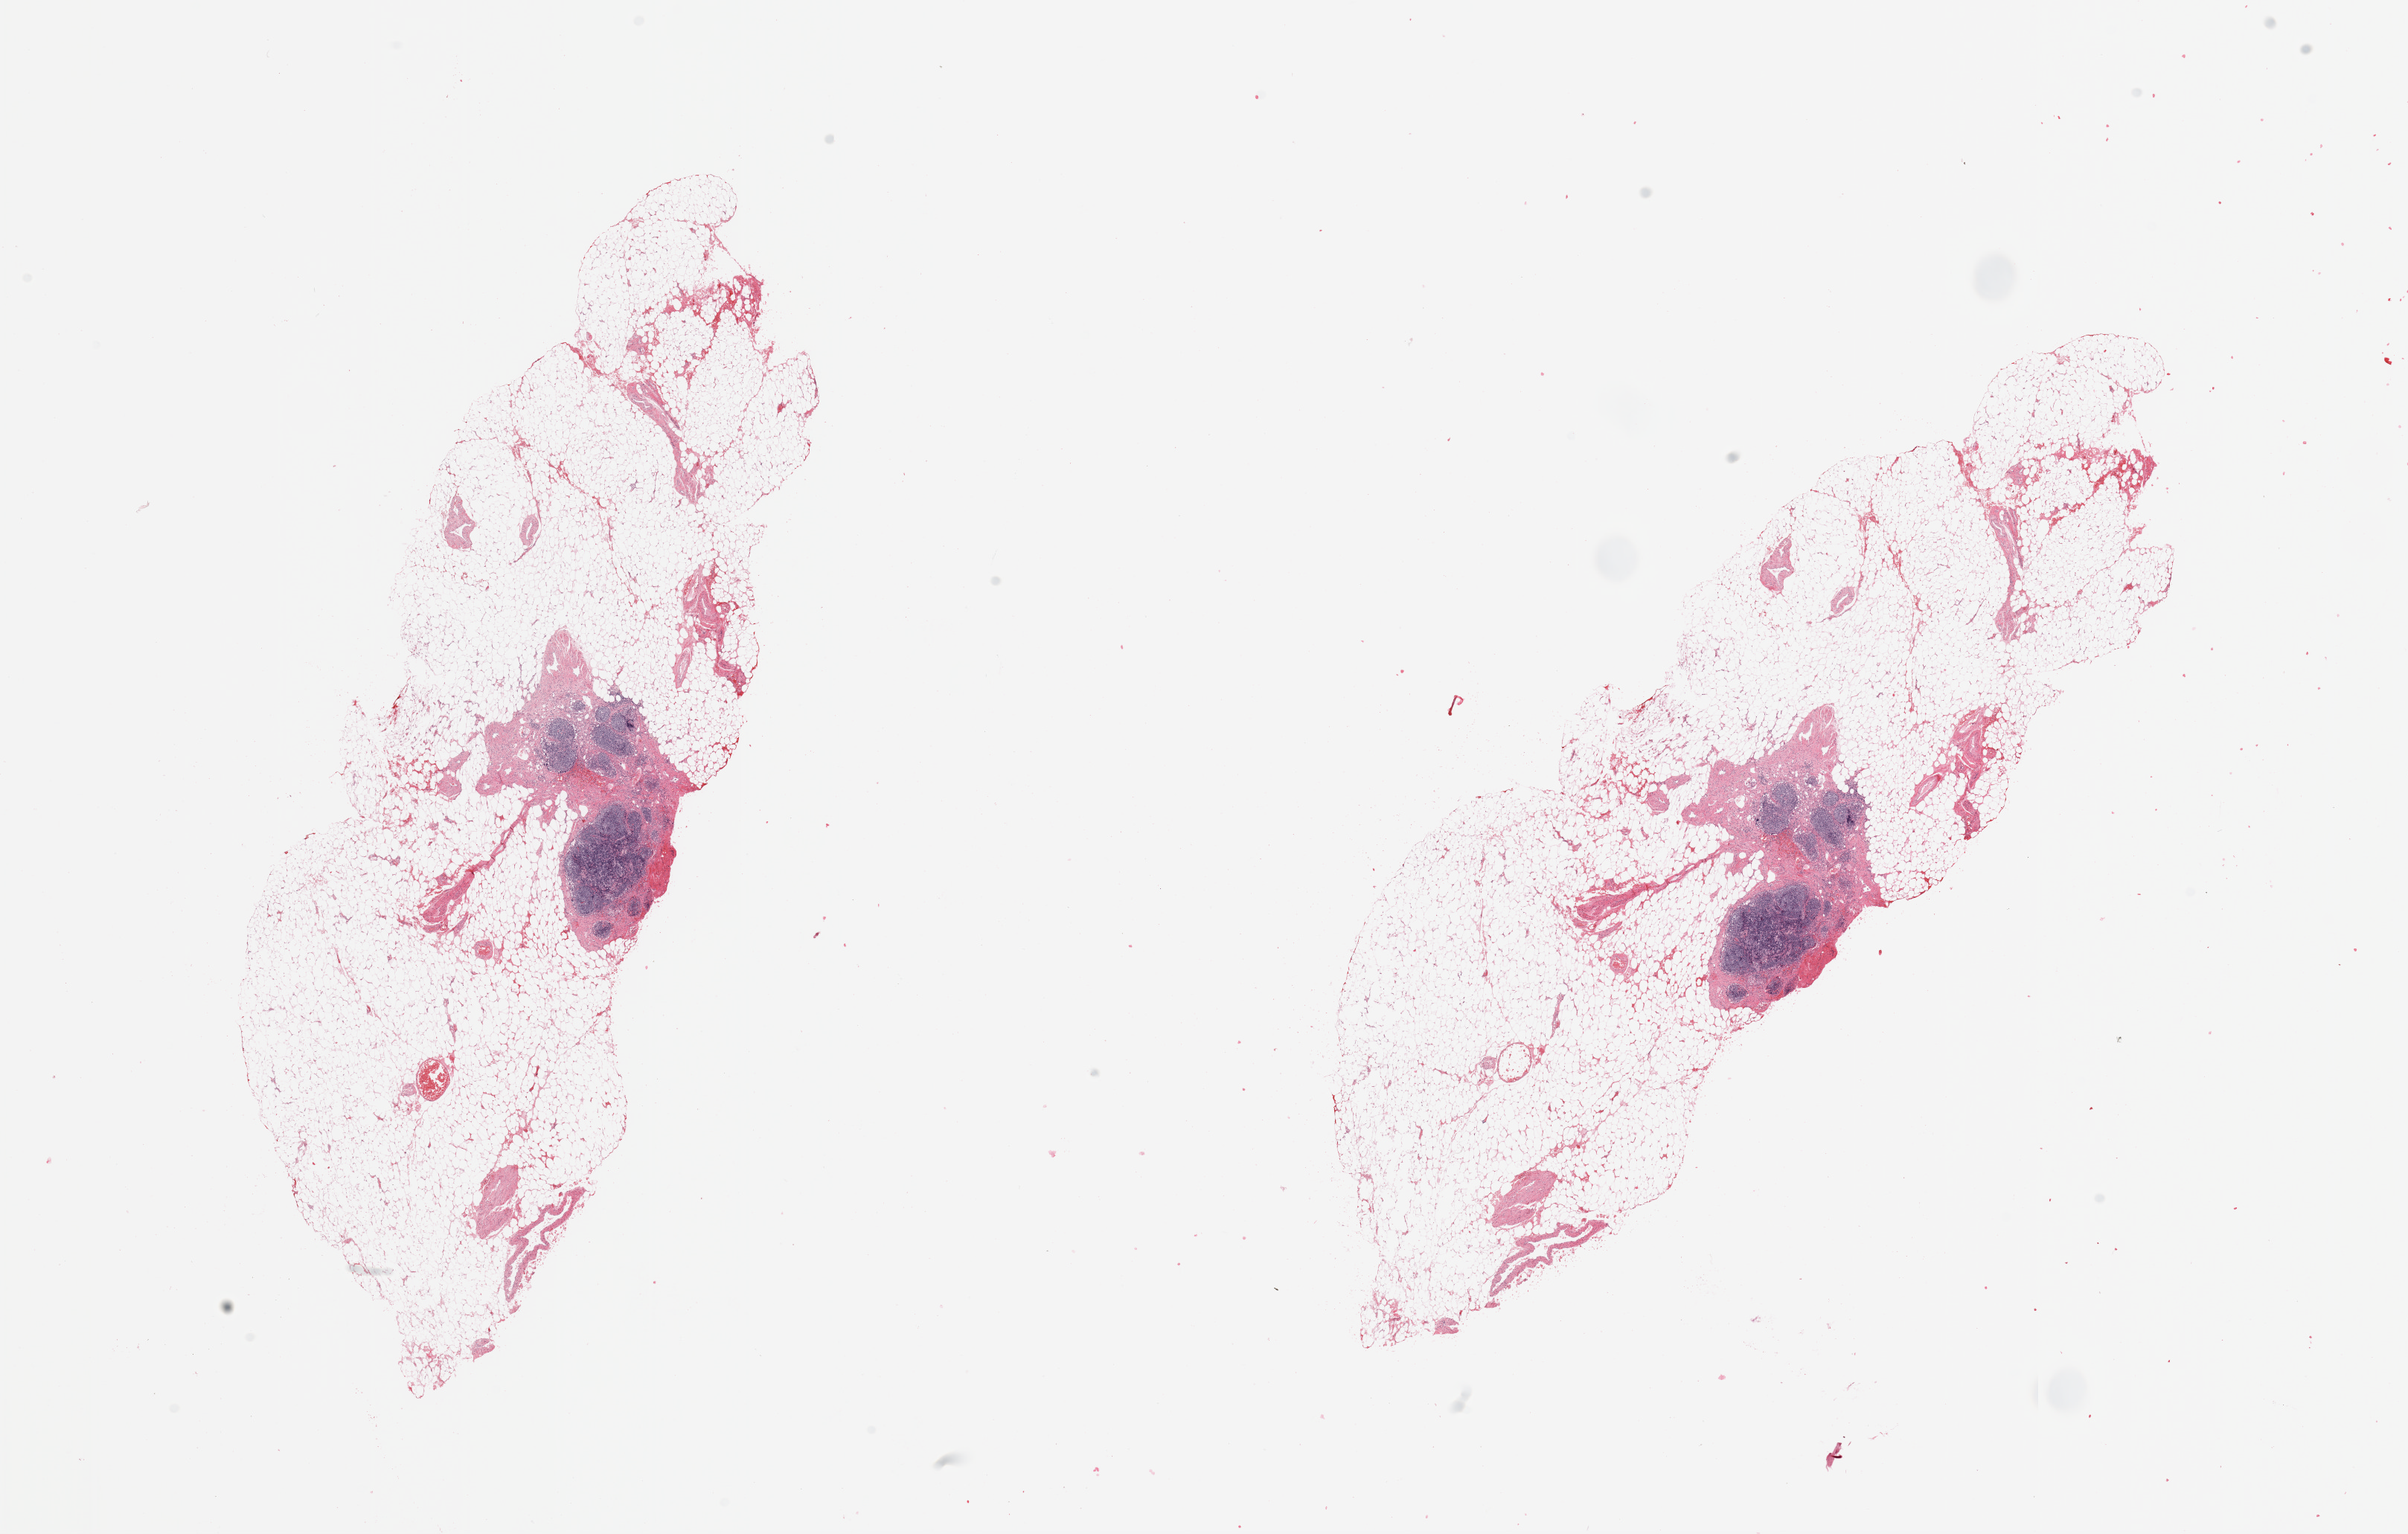
Whole-slide histology image, Hematoxylin and eosin (H&E) stained, low-resolution overview of the scanned area, about 25.6 x 16.3 mm (slide scanned at 20x); pancreas, normal (non-tumour) tissue. Male, 84 y/o.
This section: normal (non-tumour) tissue from the same patient. Patient diagnosis (cohort enrolment): ductal adenocarcinoma (pancreas).